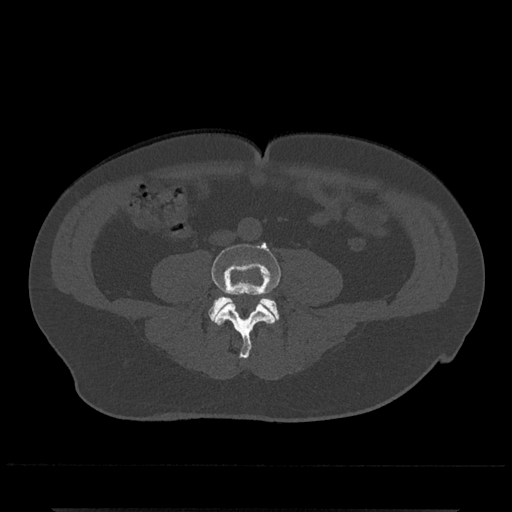
CT including the spine, one axial slice; slice 135 of 797 in the series (ordered by position); reconstruction kernel Br40s/3; 120 kVp; bone window (W 1800 / L 400 HU); 0.5 mm slice thickness; 512 × 512 image matrix, field of view 393 × 393 mm. Male patient, age 67 years. From the clinical record (not read from this slice): primary cancer: prostate.
Outlined on this slice (semi-automatically segmented with operator editing):
- L4 vertebra: bounding box (x1, y1, x2, y2) in pixels: (212, 243, 281, 359)
- L5 vertebra: (209, 296, 280, 321)